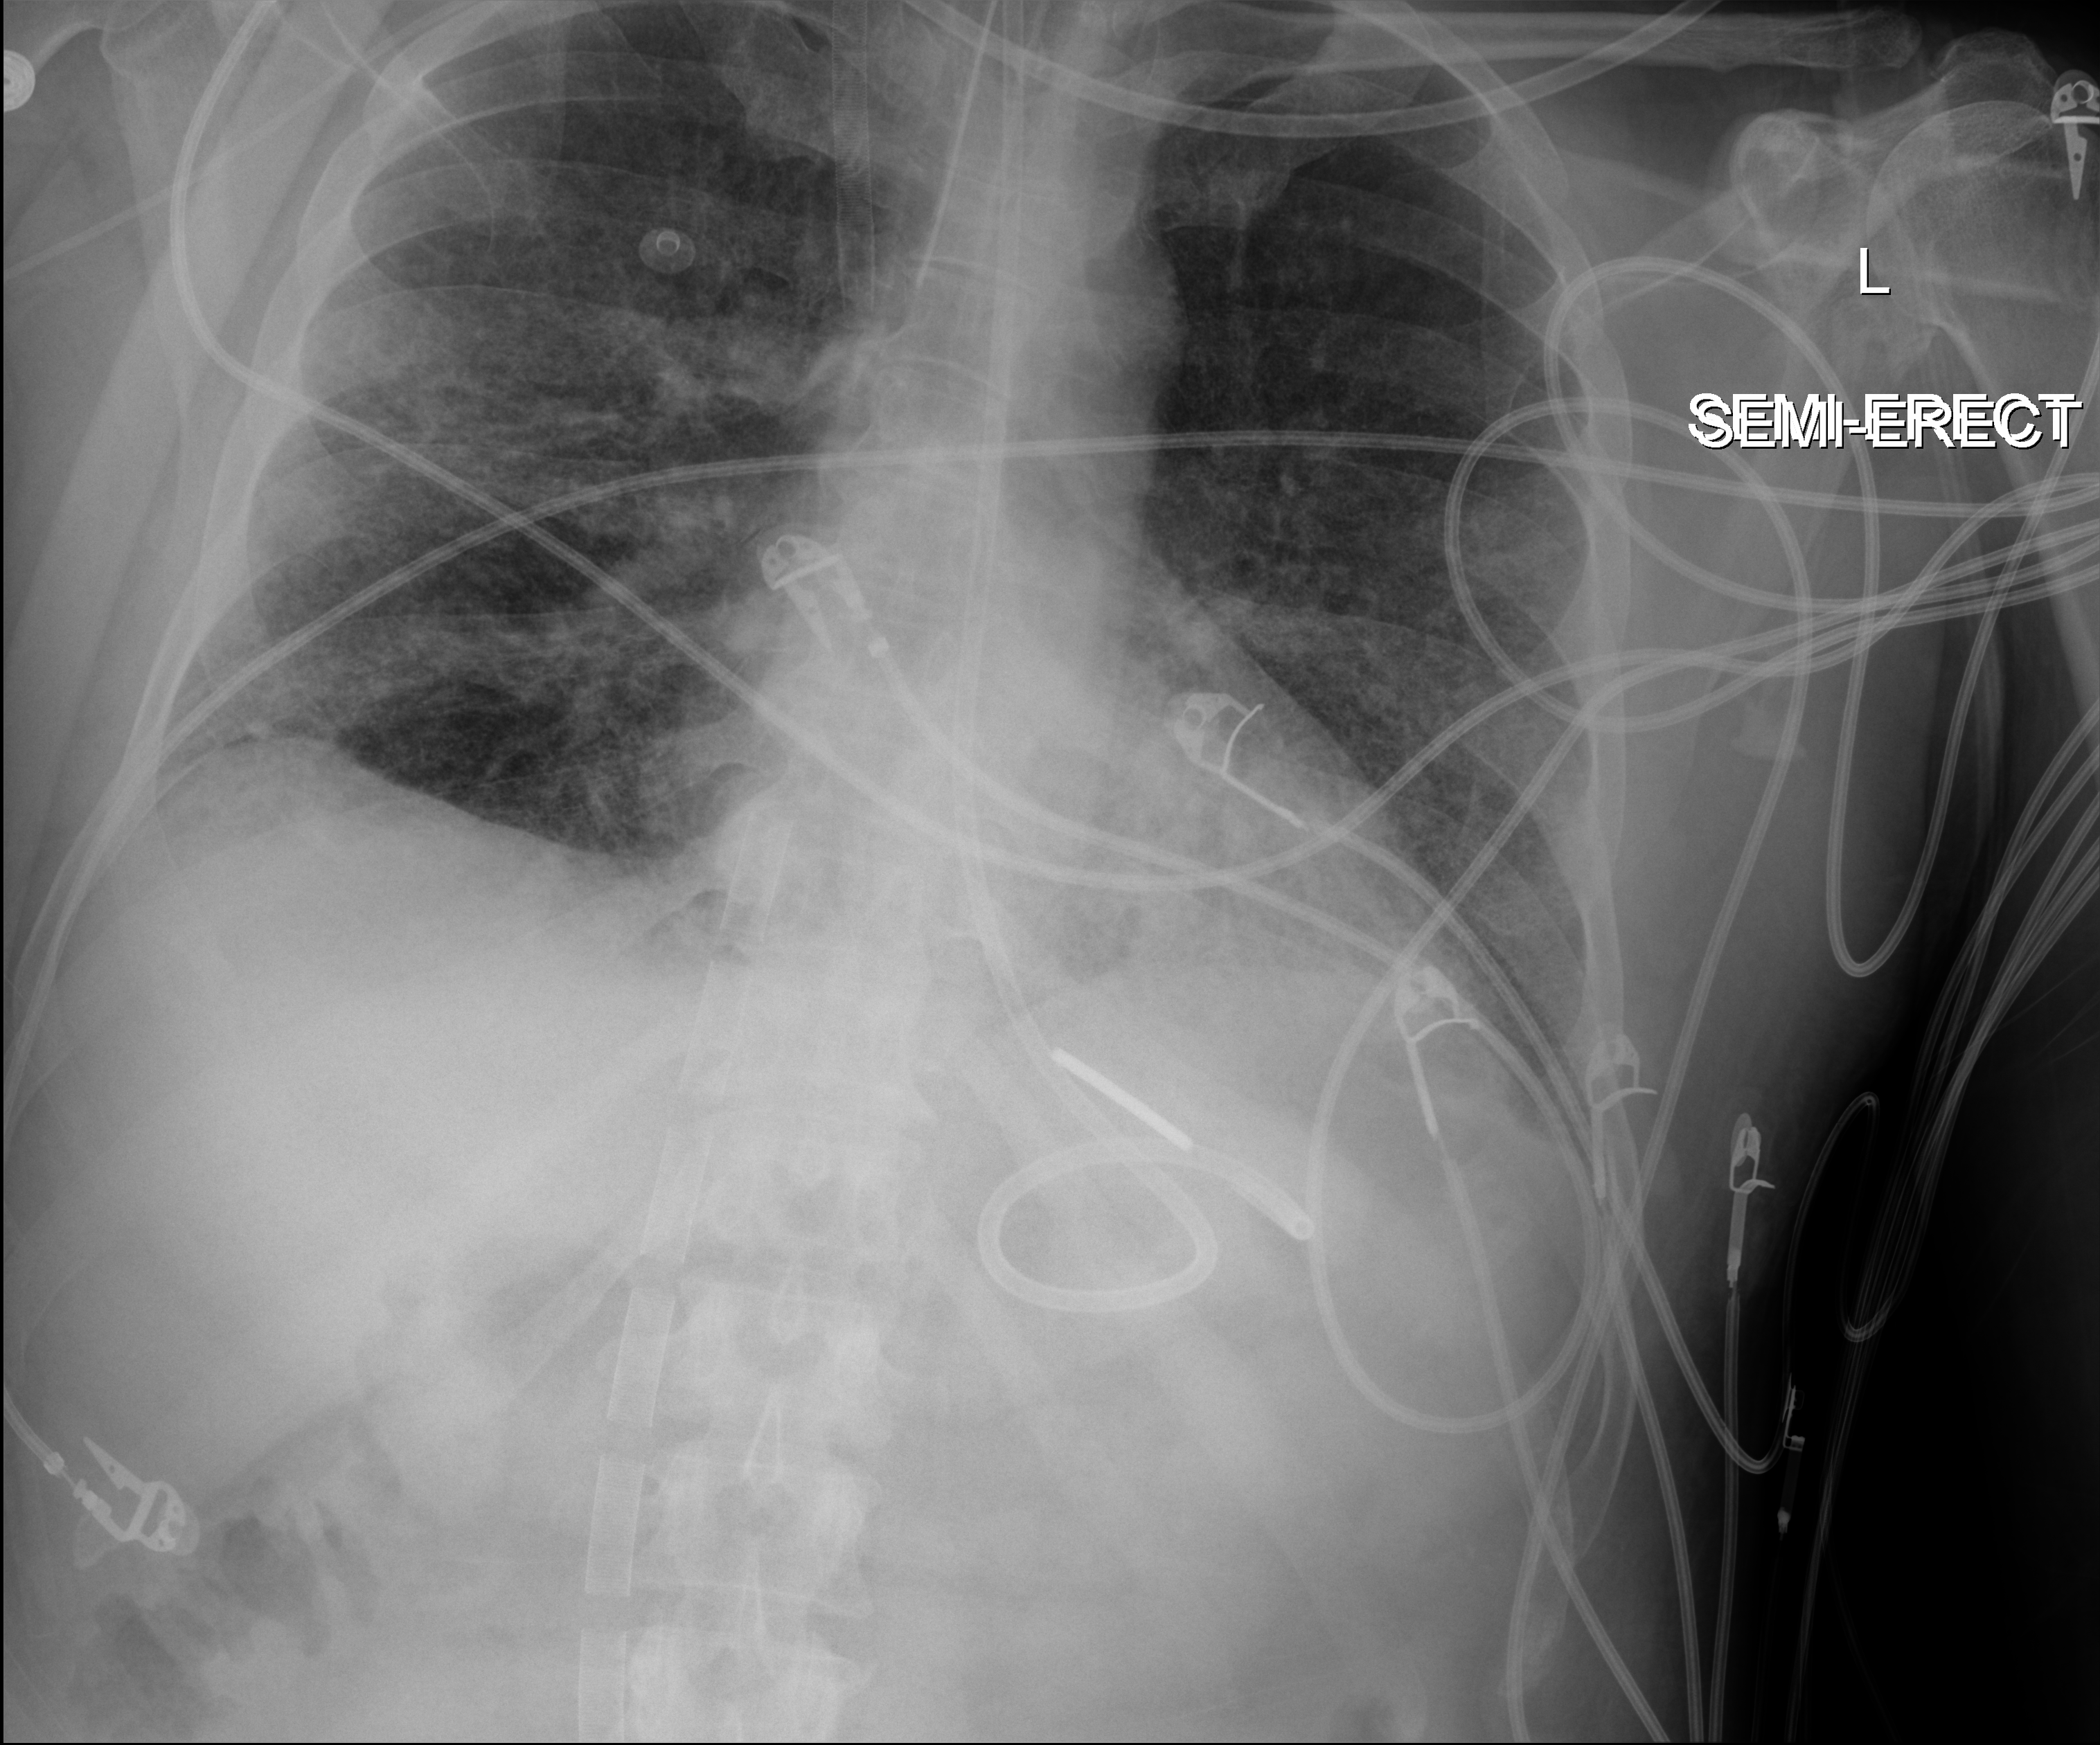
Chest X-ray (portable), anteroposterior (AP) projection. Patient hospitalised with COVID-19; male, aged 18–59 years.
Admission-level facts for this patient (not findings on this image; timing relative to this image not recorded):
- length of hospital stay: 42 days
- admitted to intensive care during this hospital stay: yes